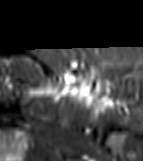
MRI of an extremity soft-tissue mass, one axial slice. Position 53 of 81 along the scan axis. STIR. MR volume resampled by the dataset authors to the PET/CT grid (not the native acquisition matrix). 3.27 mm slice thickness. 143 × 161 image matrix, field of view 140 × 157 mm. Female patient. From the clinical record (not read from this slice): histological type: myxofibrosarcoma; grade: intermediate; site of the primary tumour: left thigh.
Outlined on this slice (expert contour drawn on MRI and transferred to this co-registered scan by the dataset authors):
- gross tumour volume including surrounding oedema: box from (x=28, y=78) to (x=114, y=109) px